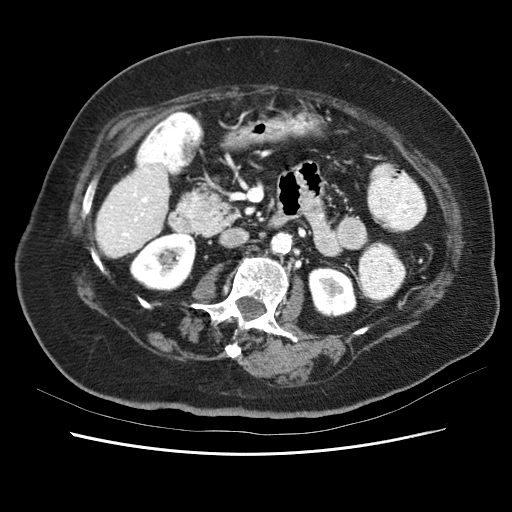
Contrast-enhanced abdominal CT (liver protocol), one axial slice; 120 kVp; soft-tissue window (W 400 / L 40 HU); 512 × 512 image matrix, field of view 340 × 340 mm. Case-level facts recorded for this patient, not image findings: diagnosis: hepatocellular carcinoma (patient treated with transarterial chemoembolisation; whether this scan precedes or follows treatment is not stated here); TNM stage (as recorded): Stage-I; Child-Pugh class: B.
Outlined on this slice (semi-automatic segmentation, software-assisted and operator-edited):
- liver parenchyma outside the tumour (the mass and vessels are separate outlines, so this box may not span the whole liver): box from (x=94, y=152) to (x=170, y=262) px
- liver vessels: (x=96, y=159)–(x=168, y=252)